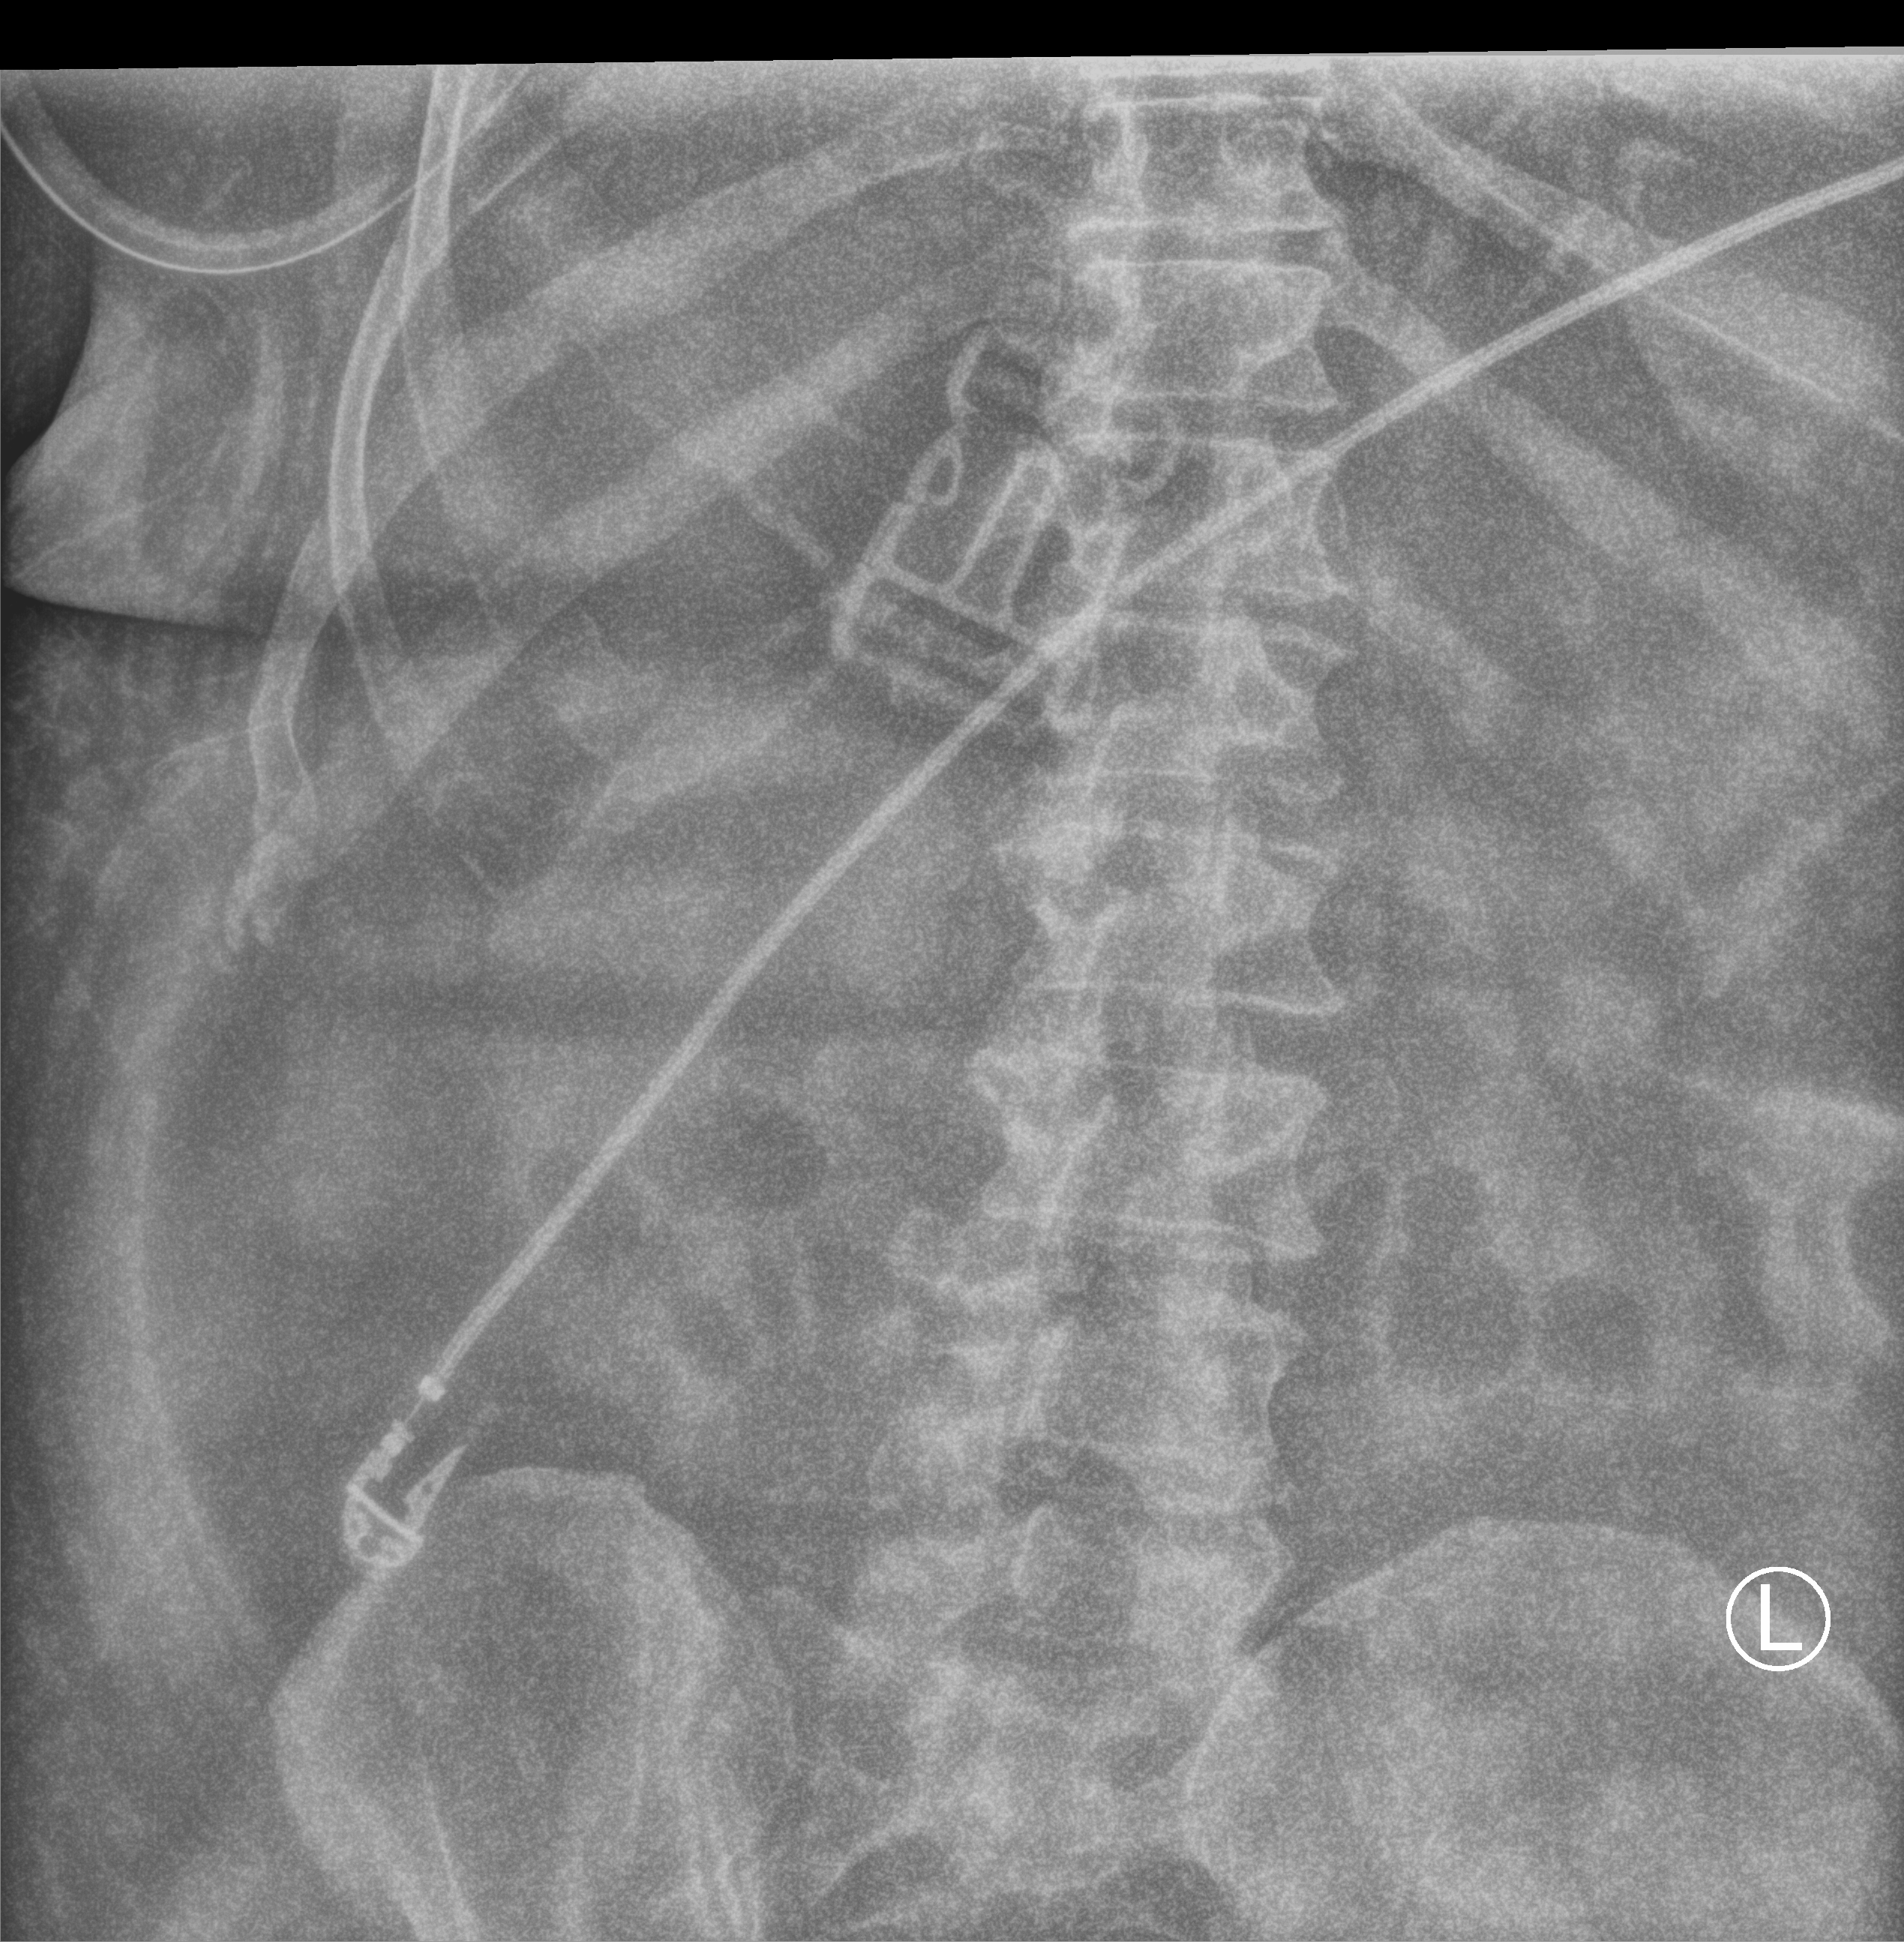
Portable abdomen radiograph; anteroposterior (AP) projection. Adult patient hospitalised with COVID-19, age 18–59 years.
Hospital-stay facts (about this admission, not read from this image; timing relative to this image not recorded): admitted to intensive care during this hospital stay: yes.